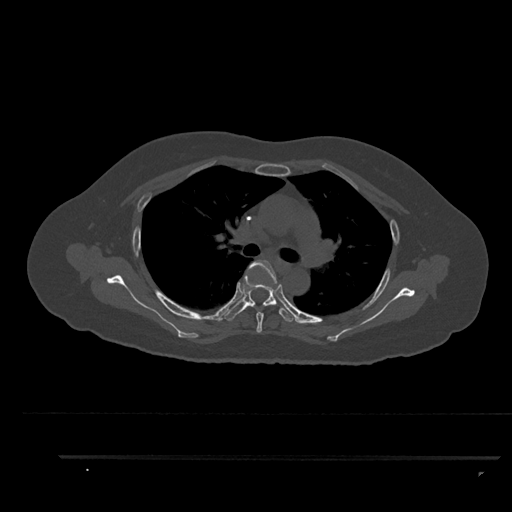
CT including the spine, one axial slice; slice 619 of 797 in the series (ordered by position); reconstruction kernel Br40s/3; 120 kVp; bone window (W 1800 / L 400 HU); 512 × 512 image matrix, field of view 408 × 408 mm. Patient: female, 44 years. Case-level facts recorded for this patient, not image findings: primary cancer: renal.
Annotated regions visible in this slice (semi-automatically segmented with operator editing):
- T4 vertebra: bounding box [x1, y1, x2, y2] px = [248, 260, 280, 333]
- T5 vertebra: [224, 275, 298, 323]